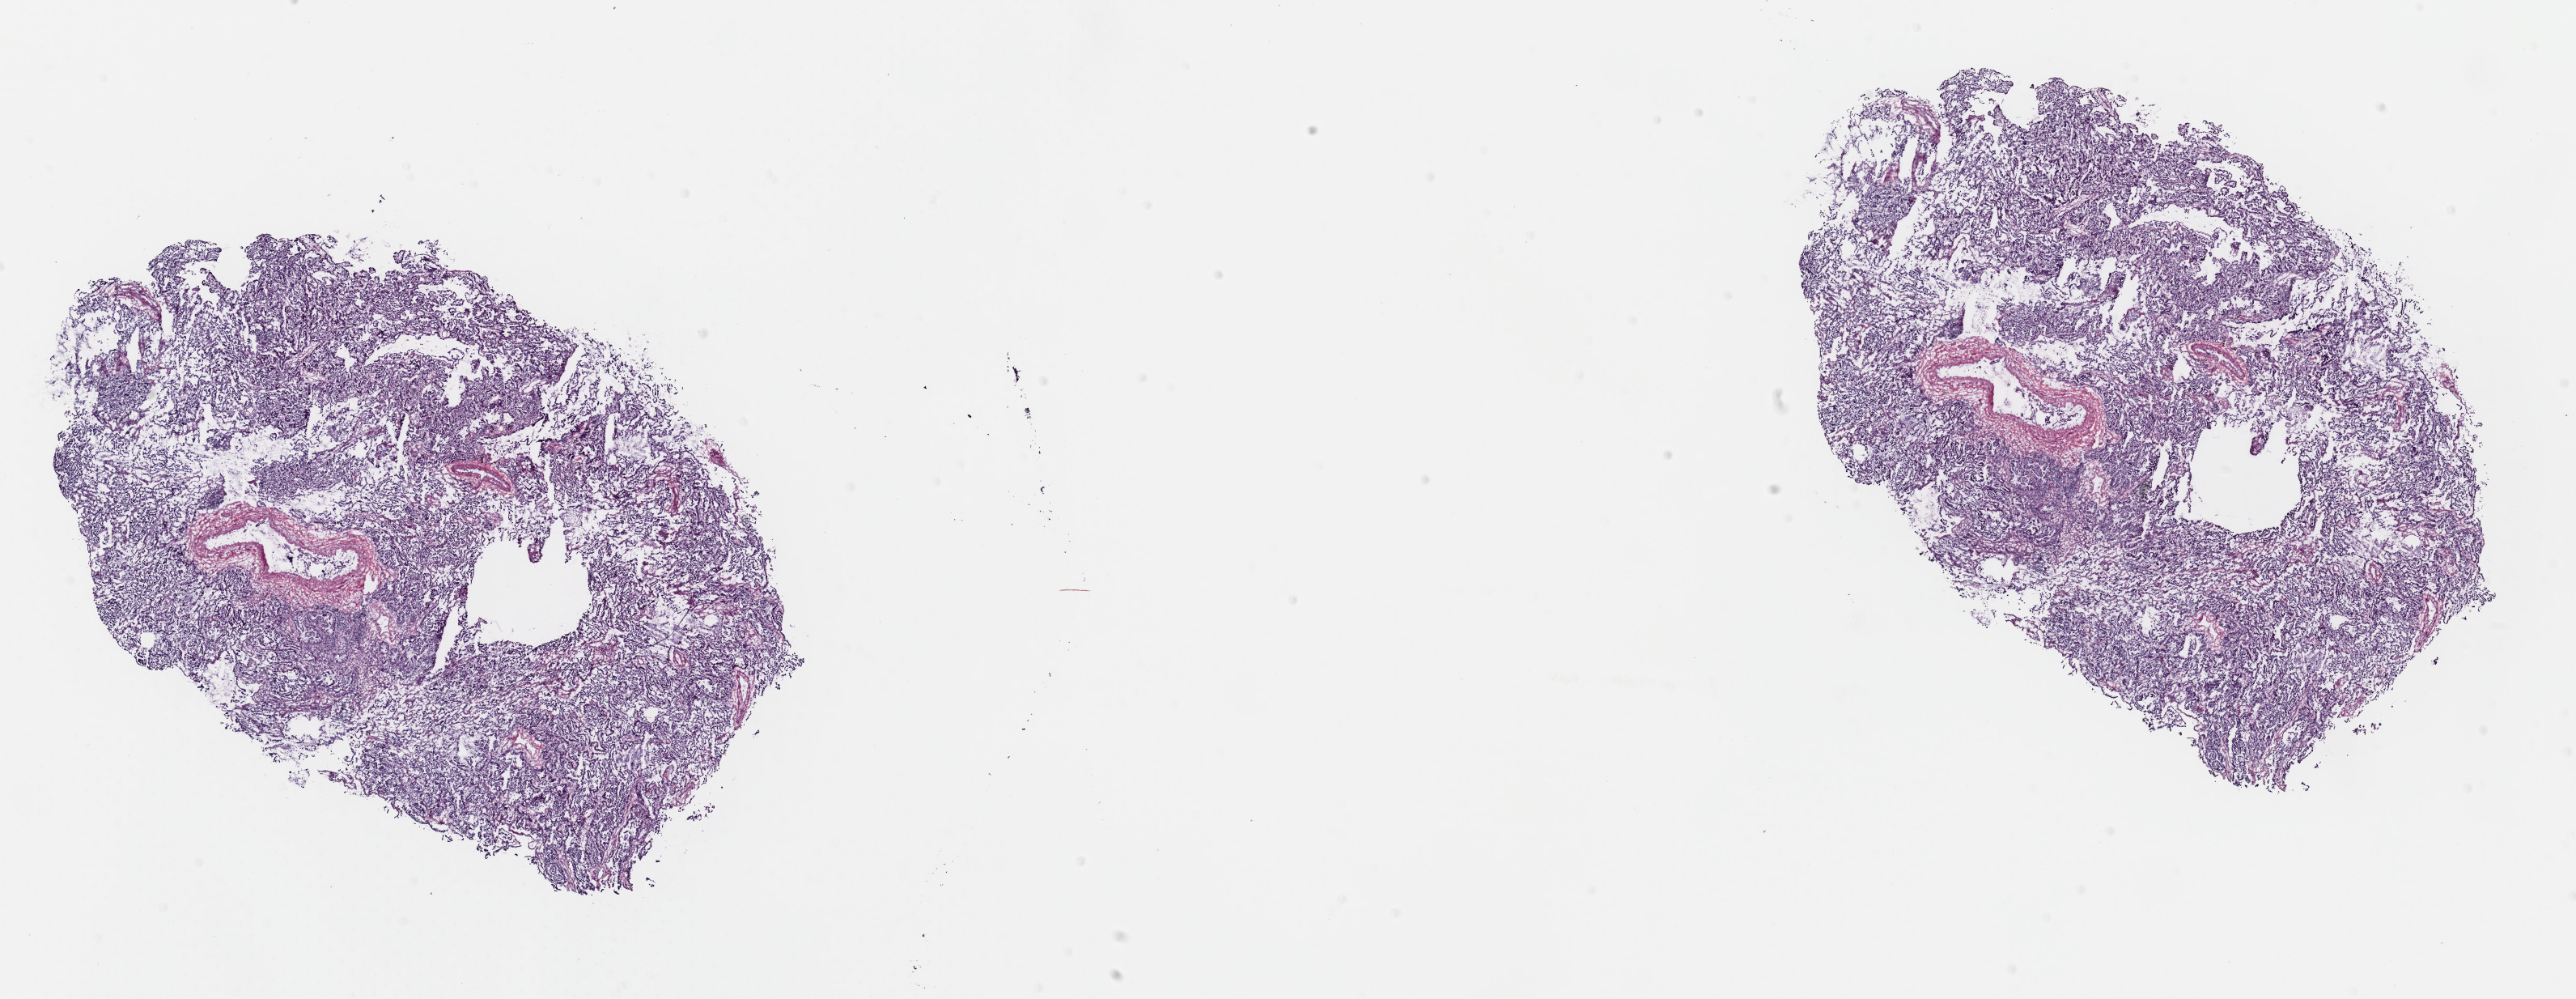
Whole-slide histology image, H&E-stained — whole scanned area (about 25.1 x 9.7 mm) shown as a low-resolution overview. Frozen section from the top of the tissue portion. Primary tumour sample from the lung. Patient: female, age at initial diagnosis 70 years. Pathologist review of this section (percent, as recorded): tumour cells 70%, tumour nuclei 70%, normal cells 0%, stromal cells 30%, necrosis 0%. Infiltration values recorded for this section: lymphocyte infiltration 5%, monocyte infiltration 5%, neutrophil infiltration 0%.
Pathologic diagnosis: Adenocarcinoma, NOS (upper lobe, lung). AJCC pathologic stage: IA (7th edition).